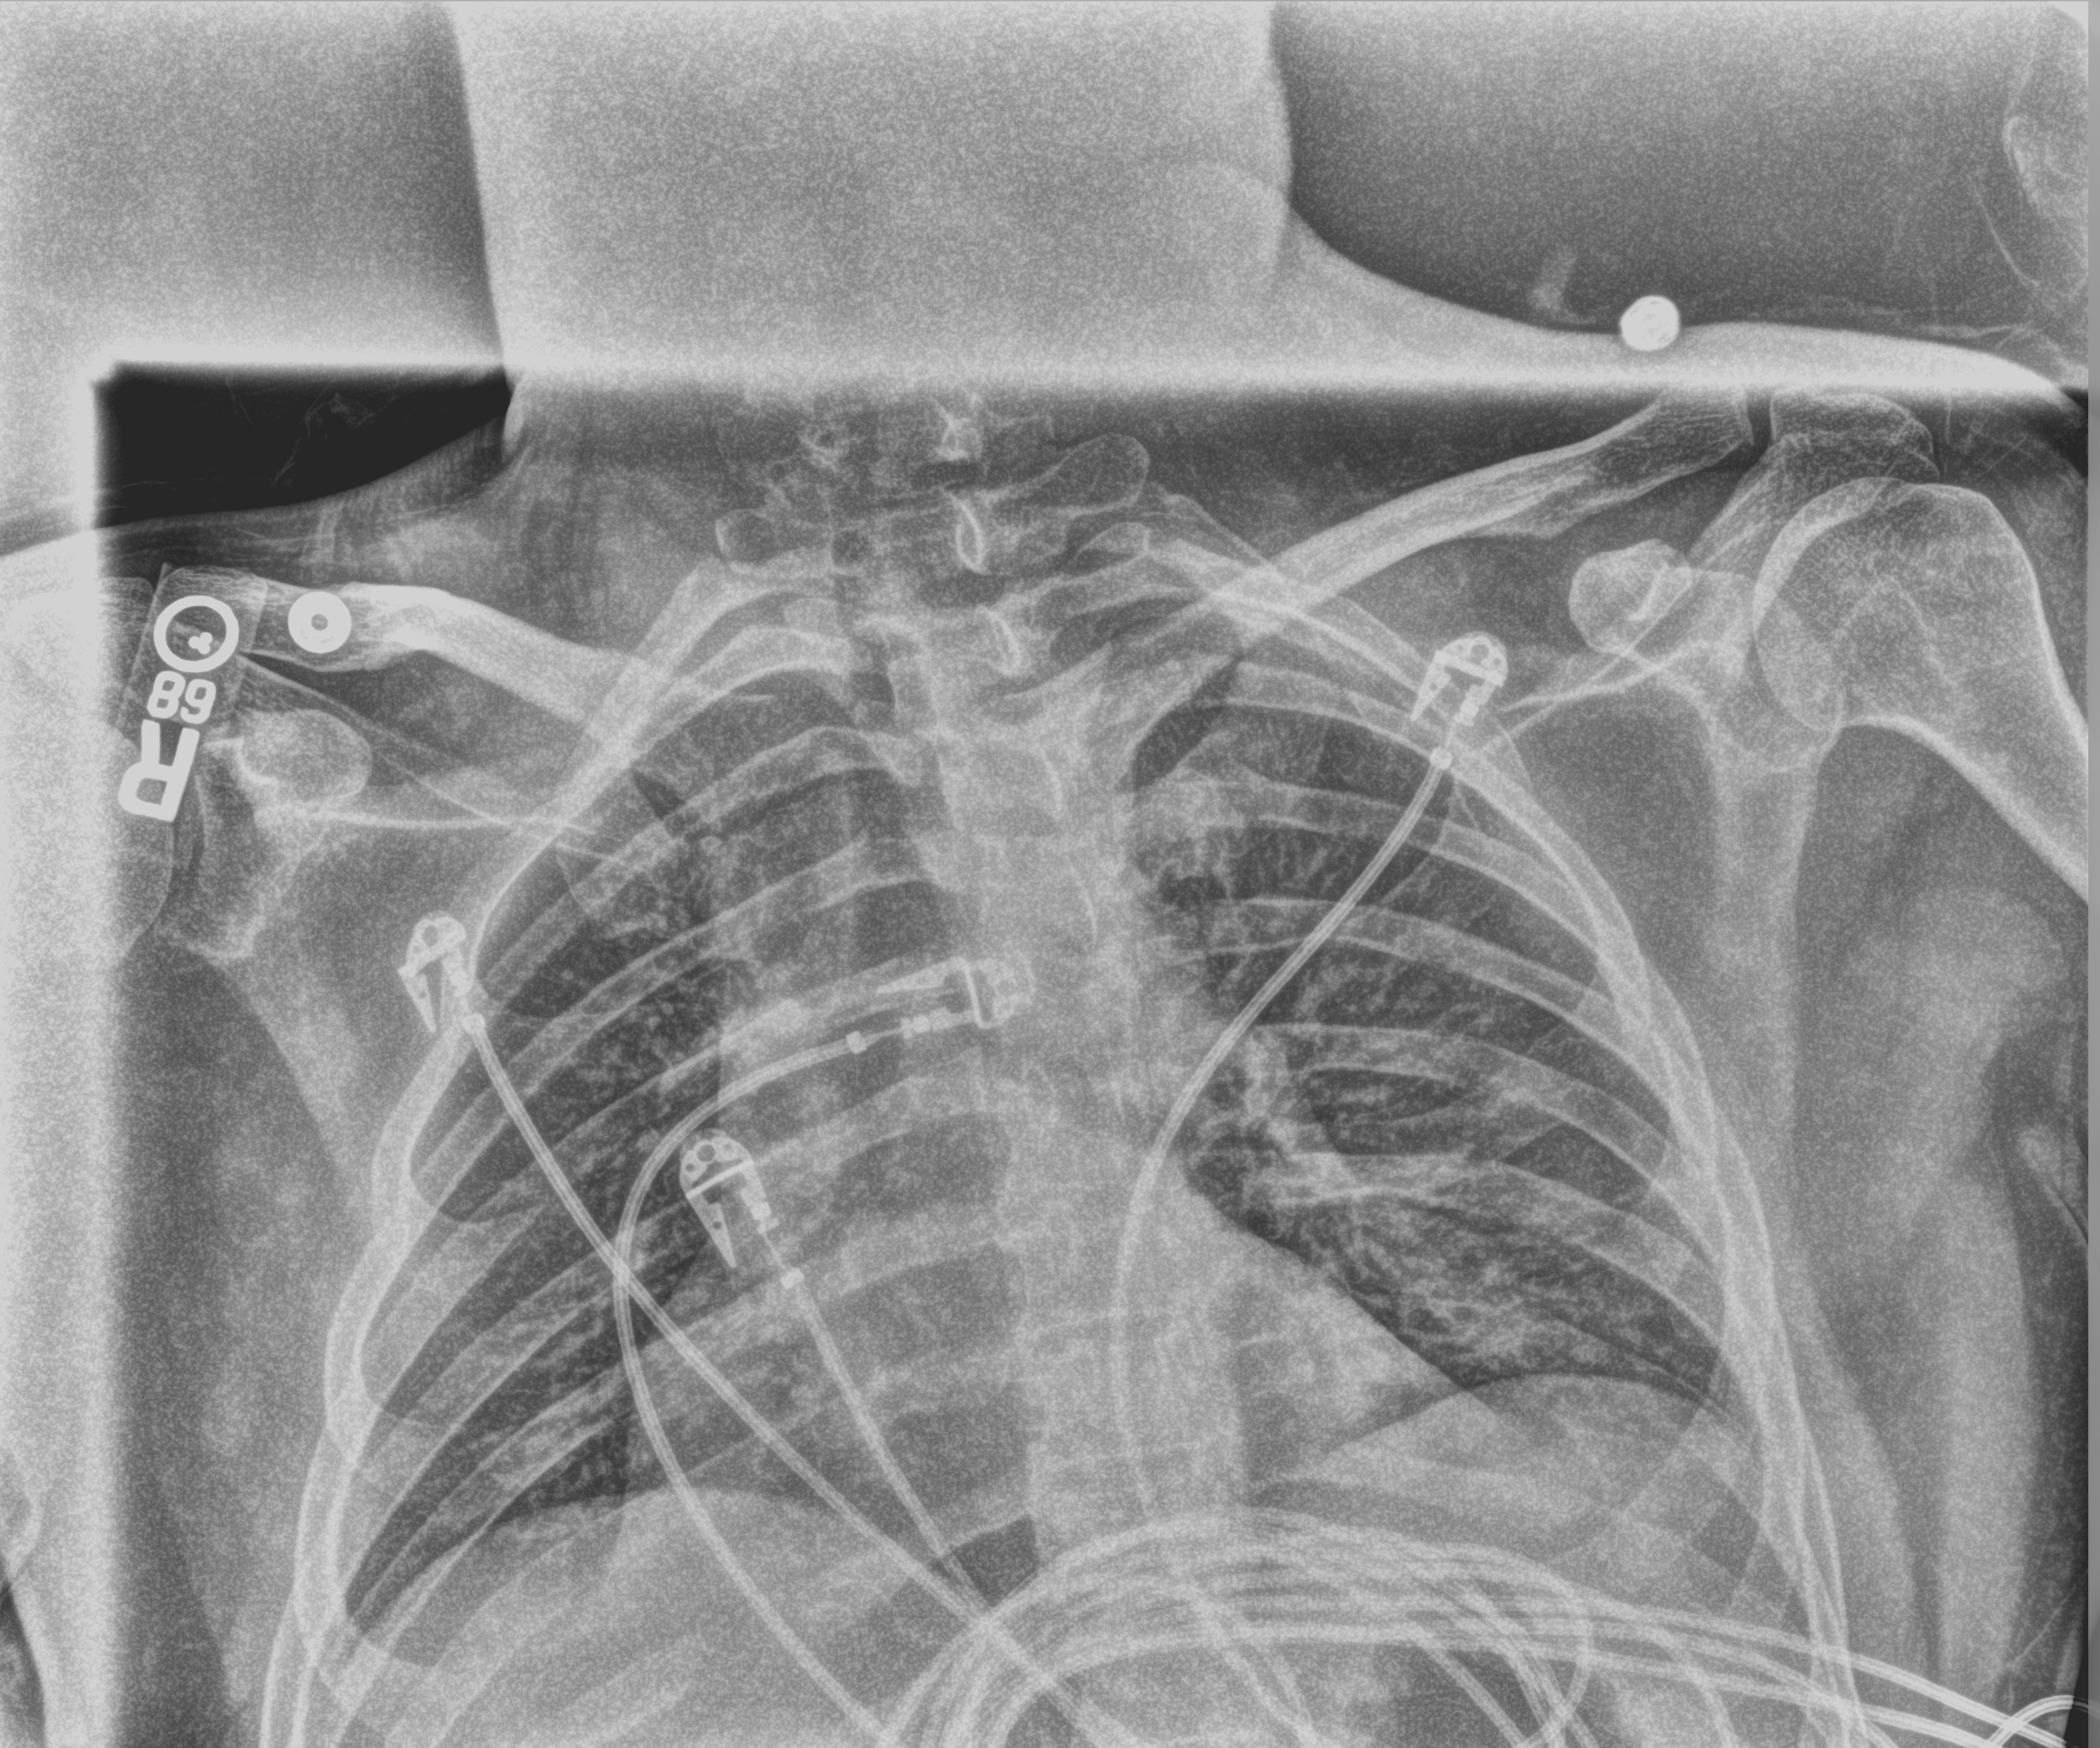
Chest X-ray (portable); anteroposterior (AP) projection. Patient hospitalised with COVID-19; male, aged 18–59 years.
Admission-level facts for this patient (not findings on this image; timing relative to this image not recorded): admitted to intensive care during this hospital stay: yes; diabetes (admission record): no.